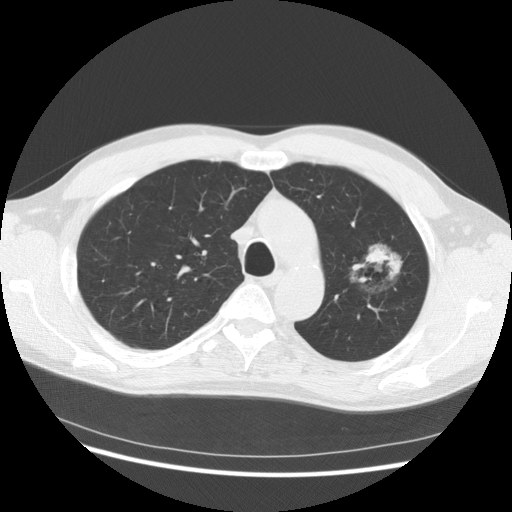
Axial slice from a low-dose chest CT screening exam, third screening round (two years after baseline), lung window (W 1500 / L -600 HU), 140 kVp, slice 104 of 145 in the series, 512 × 512 image matrix. Male participant, aged 61 years at enrolment. Former smoker at enrolment.
• Expert reader's lesion annotation, bounding box [x1, y1, x2, y2] px = [332, 230, 411, 310].
• Screening reader's record for this exam (one nodule recorded; not confirmed to be the boxed lesion): non-calcified nodule or mass ≥4 mm, left upper lobe, 37 × 33 mm, poorly defined margins, mixed attenuation, pre-existing on the prior screen: yes; interval growth: yes.
• Participant outcome: lung cancer diagnosed 361 days after this screen — bronchiolo-alveolar adenocarcinoma, NOS, left upper lobe, well differentiated (G1), stage IB (AJCC 6th edition), 44 mm at pathology.